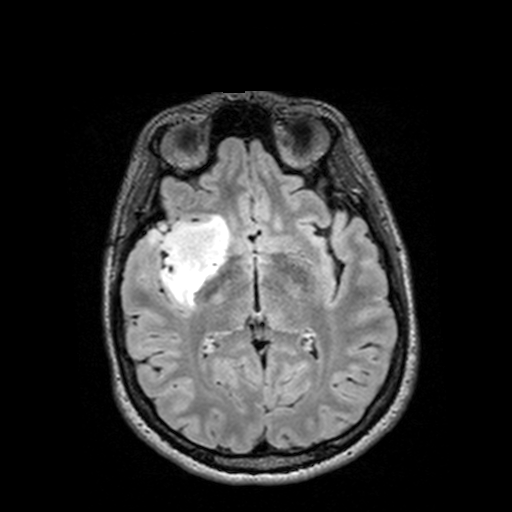
Brain MRI from a brain-tumour surgery series, one axial slice; slice 74 of 144 in the series (ordered by position); T2 FLAIR; 512 × 512 image matrix, field of view 250 × 250 mm. From the clinical record (not read from this slice): histopathology: Astrocytoma; WHO grade: 3; IDH mutation: yes; tumour location: Right Insular Temporal.
Outlined on this slice (expert manual segmentation):
- tumour: box from (x=126, y=217) to (x=232, y=303) px